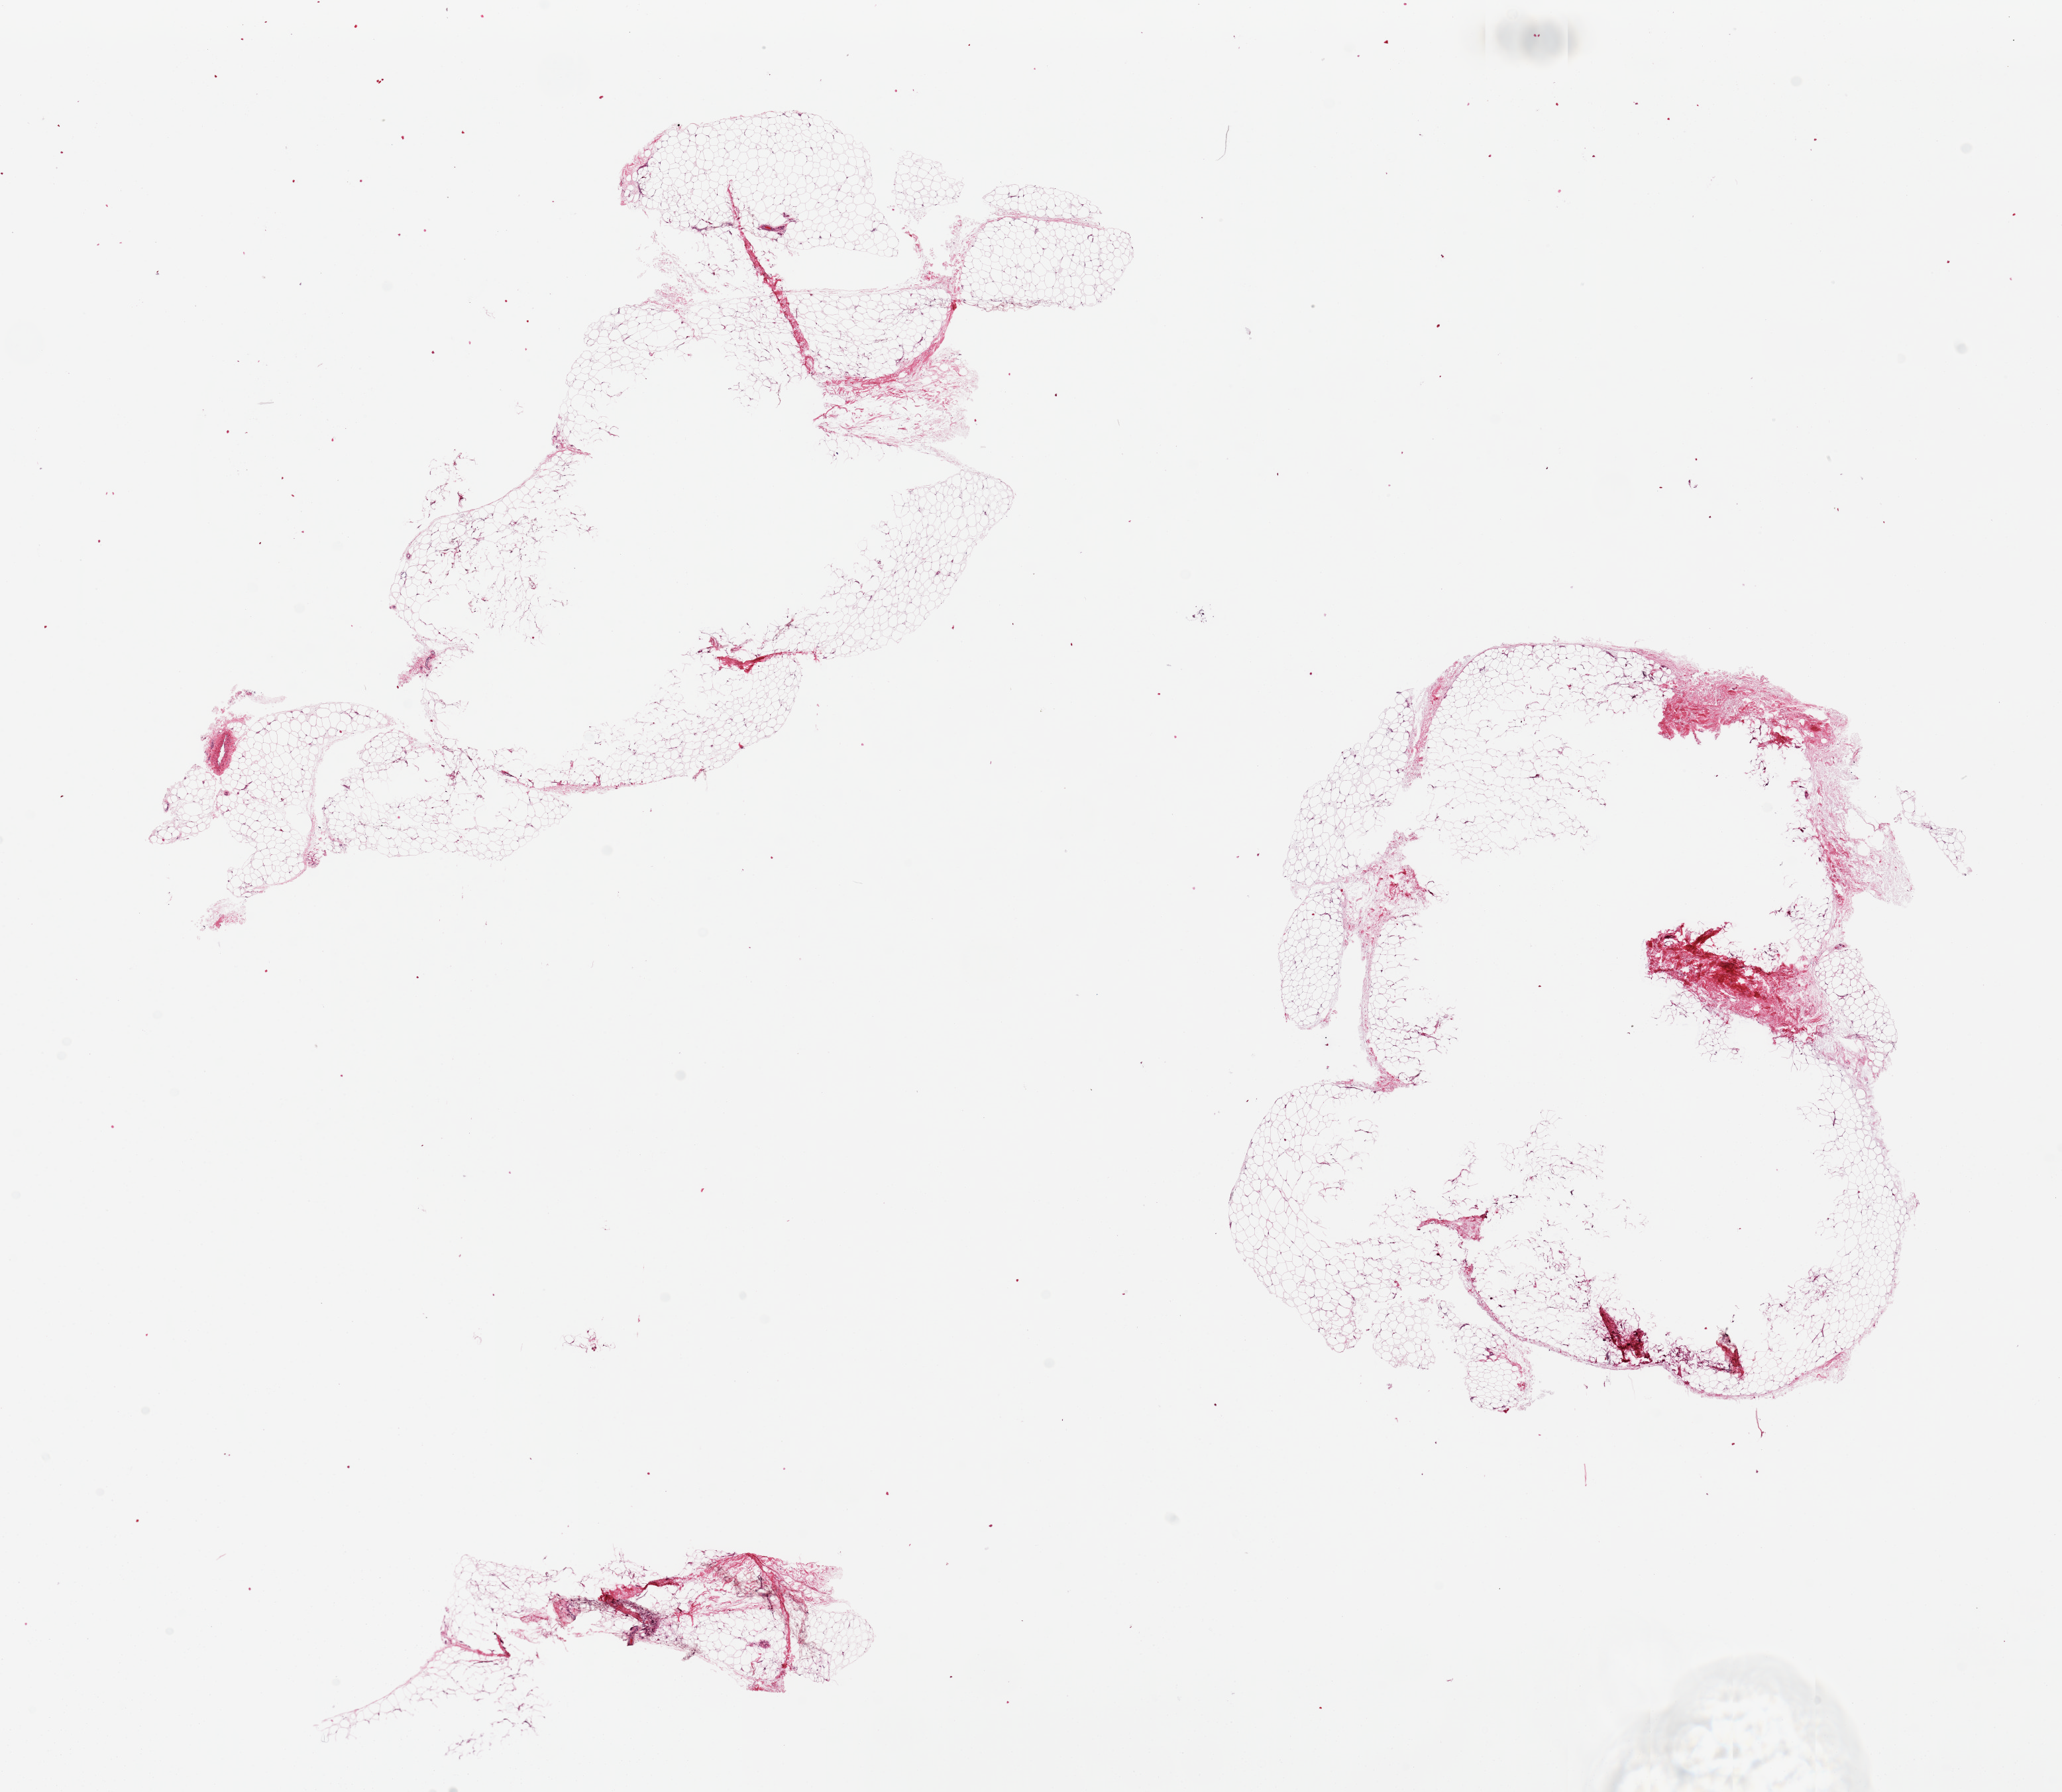
Digitized haematoxylin and eosin-stained section — a low-resolution overview of the entire scanned area, about 24.6 x 21.4 mm, PAXgene-fixed, paraffin-embedded tissue, section of adipose tissue (target tissue), tissue donor sample. Donor: male.
Review note (as recorded): 2 ~9x8mm pieces. Central ~75% of both is unfixed with large holes.